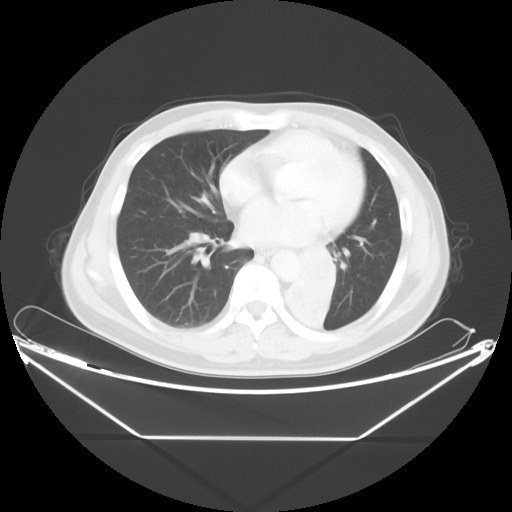
Chest CT, one axial slice. Slice 20 of 48 in the series (ordered by position). Reconstruction kernel STANDARD. 120 kVp. Lung window (W 1500 / L -600 HU). 5 mm slice thickness. 512 × 512 image matrix, field of view 438 × 438 mm. Male patient, age 58 years. Case-level facts recorded for this patient, not image findings: clinical TNM (as recorded): T3 N3 M0.
Outlined on this slice (rectangle marked by the reading radiologist):
- lung tumour (recorded histology: squamous cell carcinoma): bounding box (x1, y1, x2, y2) in pixels: (274, 233, 345, 346)